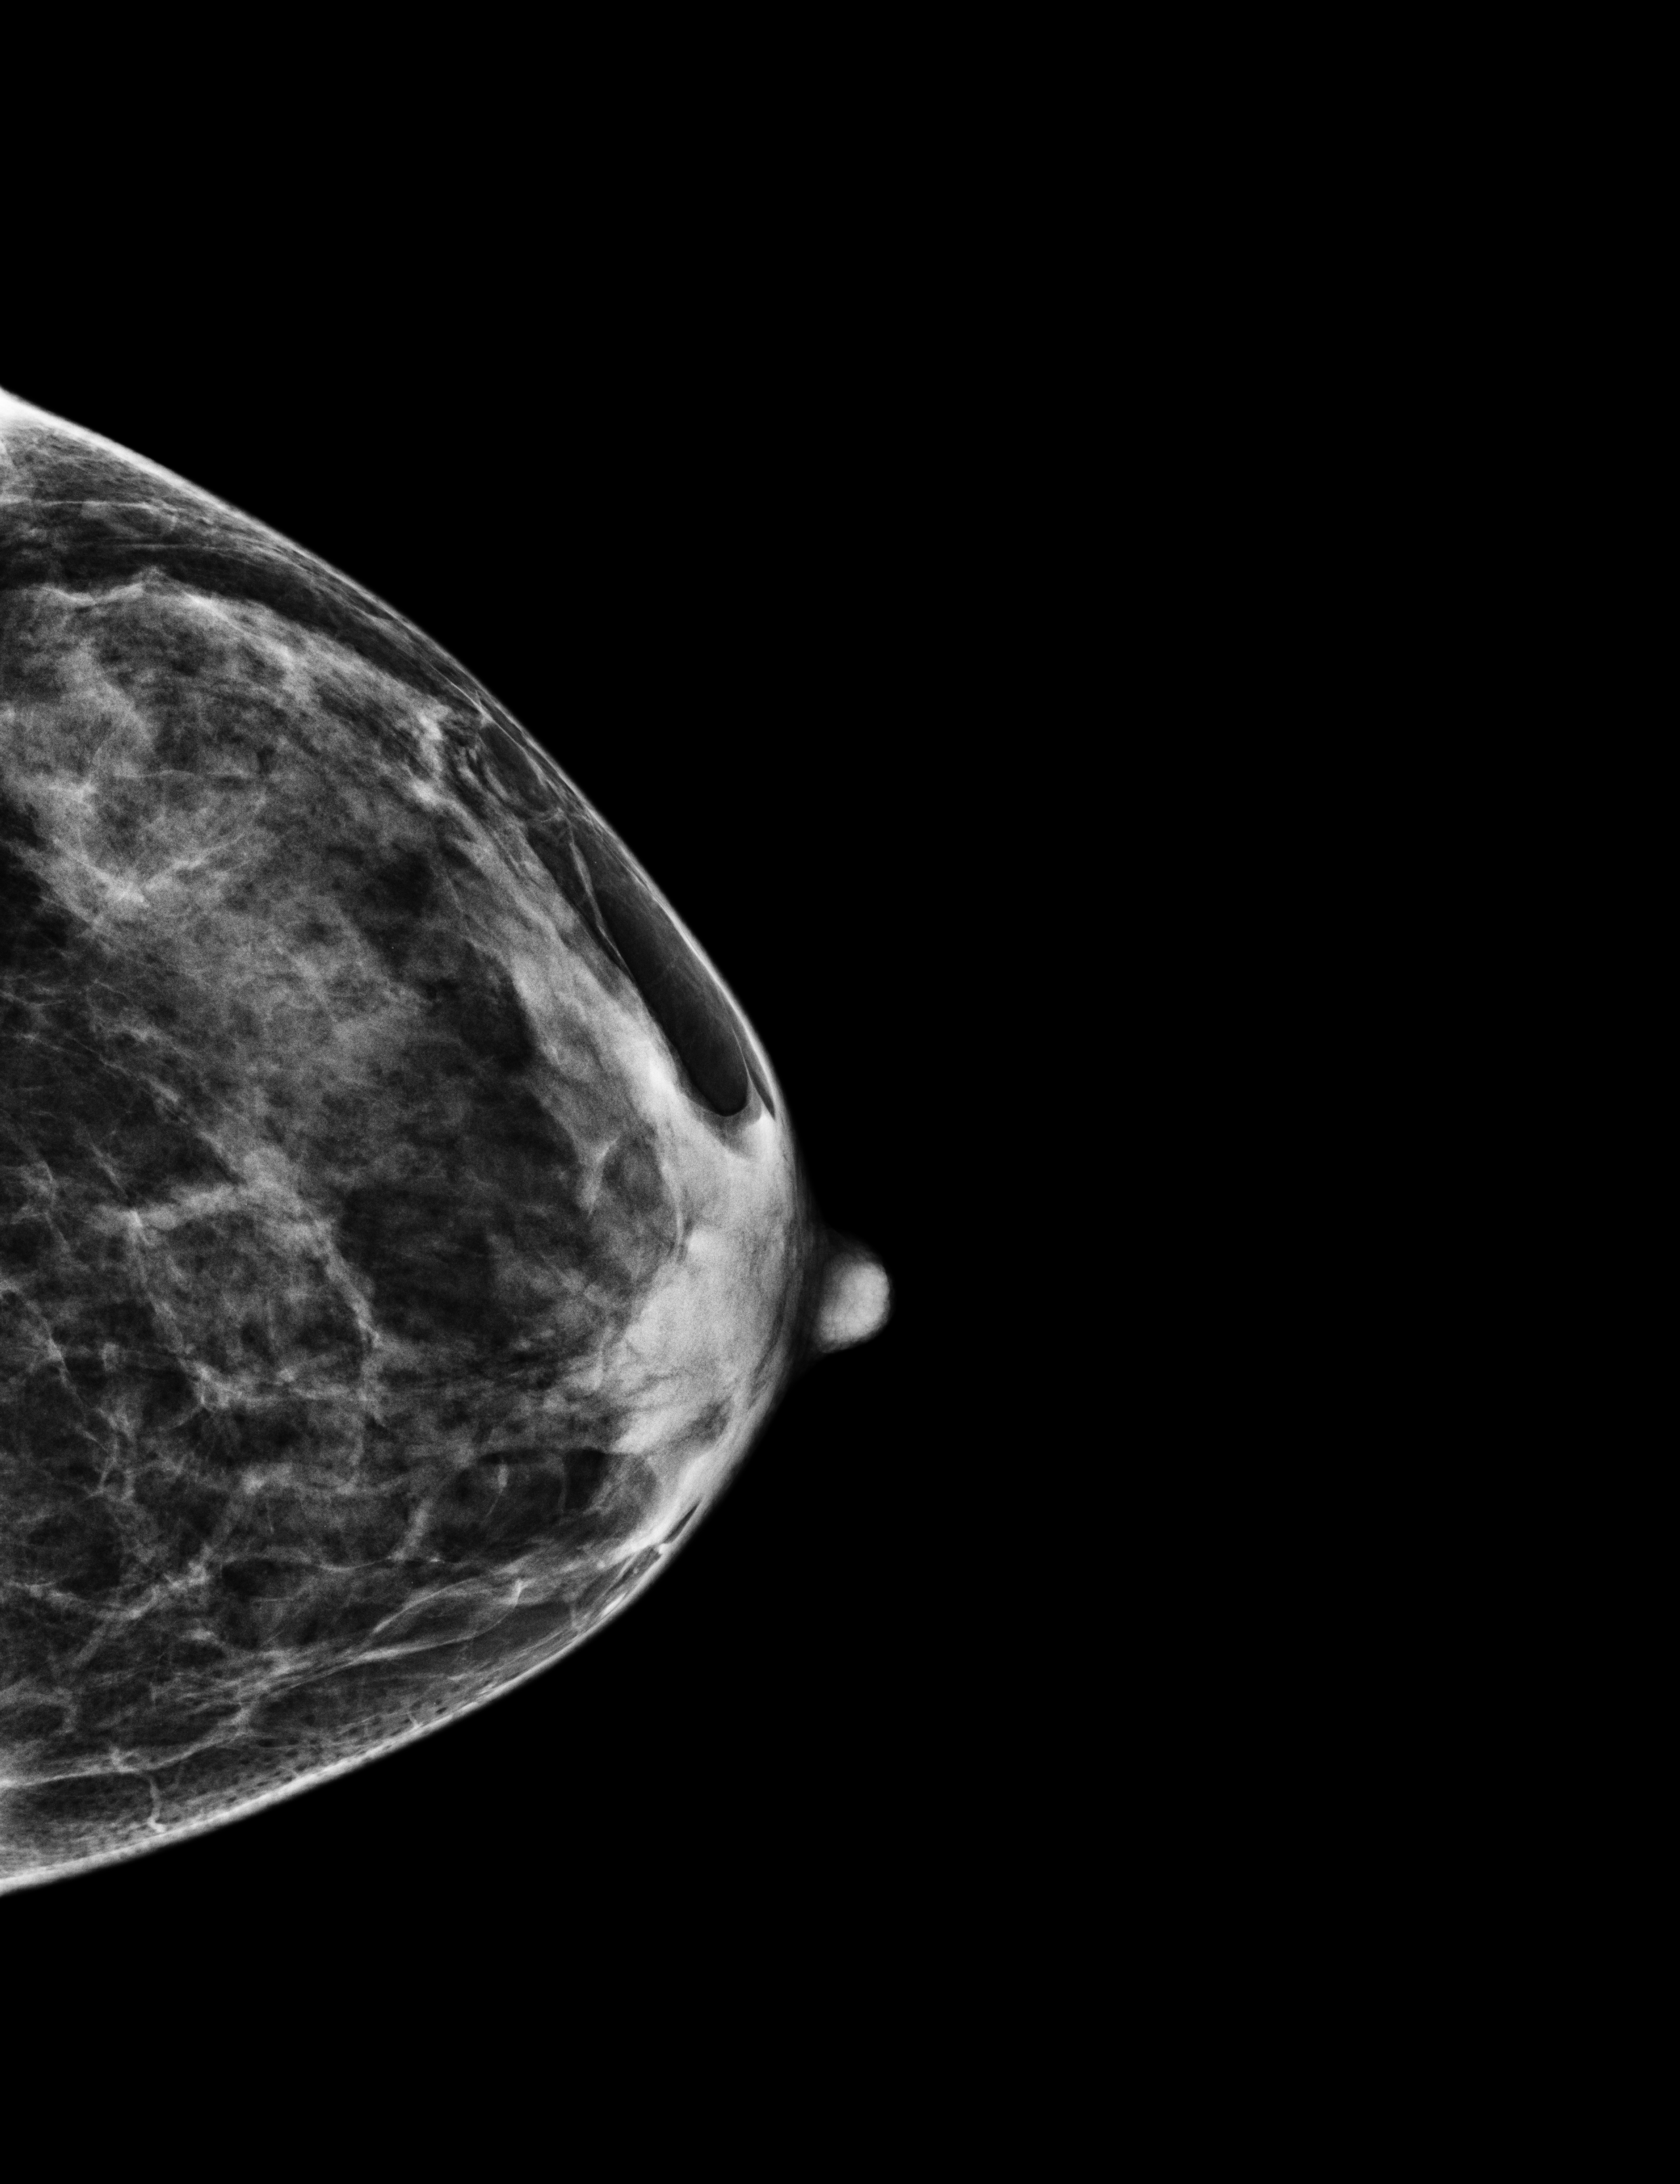
Screening examination, system: Selenia Dimensions. Female patient, age 56 years.
Image type: full-field digital mammogram. Breast: left. Projection: craniocaudal (CC) view.